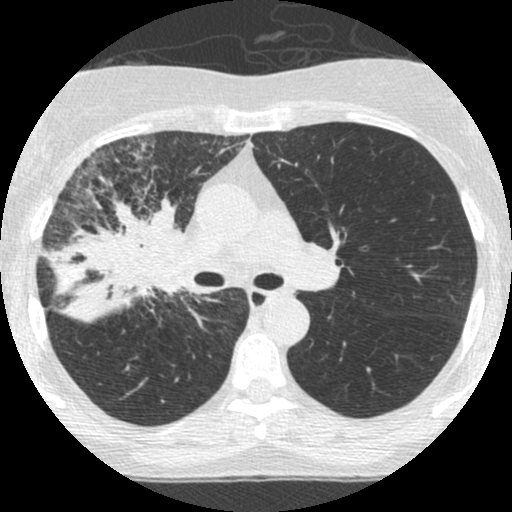
Low-dose screening chest CT, one axial slice. Position 162 of 253 along the scan axis. Reconstruction kernel STANDARD. Lung window (W 1500 / L -600 HU). 1.25 mm slice thickness. 512 × 512 image matrix, field of view 294 × 294 mm.
Structures marked on this image (manually delineated by an expert):
- lesion 2 (tumor, hilum of right lung): bounding box <42,197,187,325> (left, top, right, bottom; pixels)